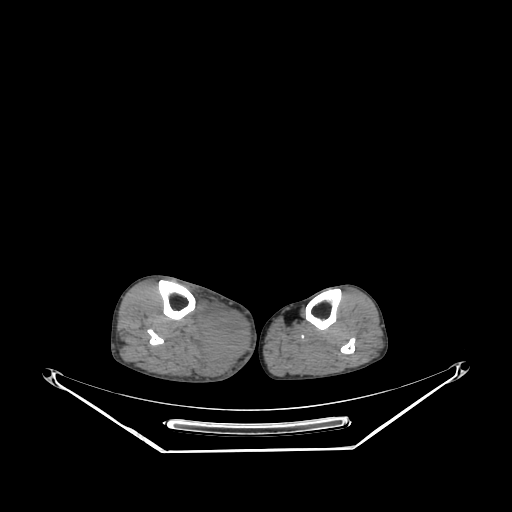
CT of an extremity soft-tissue mass (from a PET/CT study), one axial slice; position 131 of 267 along the scan axis; reconstruction kernel SOFT; soft-tissue window (W 400 / L 40 HU); 3.75 mm slice thickness; 512 × 512 image matrix. Male patient. Case-level facts recorded for this patient, not image findings: histological type: pleiomorphic liposarcoma; grade: high; site of the primary tumour: right calf.
Annotated regions visible in this slice (expert contour drawn on MRI and transferred to this co-registered scan by the dataset authors):
- gross tumour volume including surrounding oedema: bounding box <199,302,252,378> (left, top, right, bottom; pixels)
- gross tumour volume (mass): <199,306,252,362>